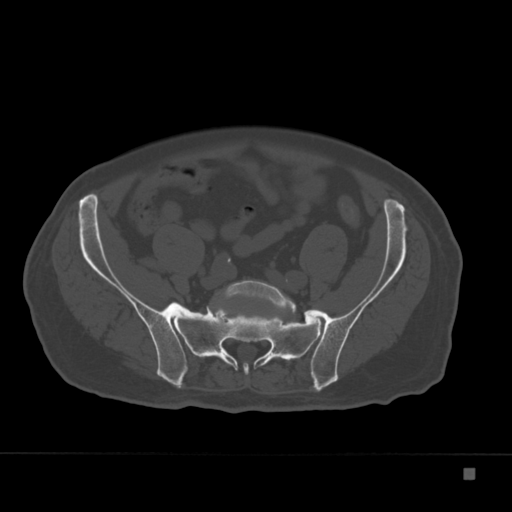
CT including the spine, one axial slice; slice 8 of 332 in the series (ordered by position); reconstruction kernel Br40s; 120 kVp; bone window (W 1800 / L 400 HU); 1.5 mm slice thickness; 512 × 512 image matrix, field of view 389 × 389 mm. Patient: male, 72 years. Case-level facts recorded for this patient, not image findings: primary cancer: skeletal.
Structures marked on this image (semi-automatic segmentation, software-assisted and operator-edited):
- L5 vertebra: box from (x=222, y=280) to (x=296, y=313) px